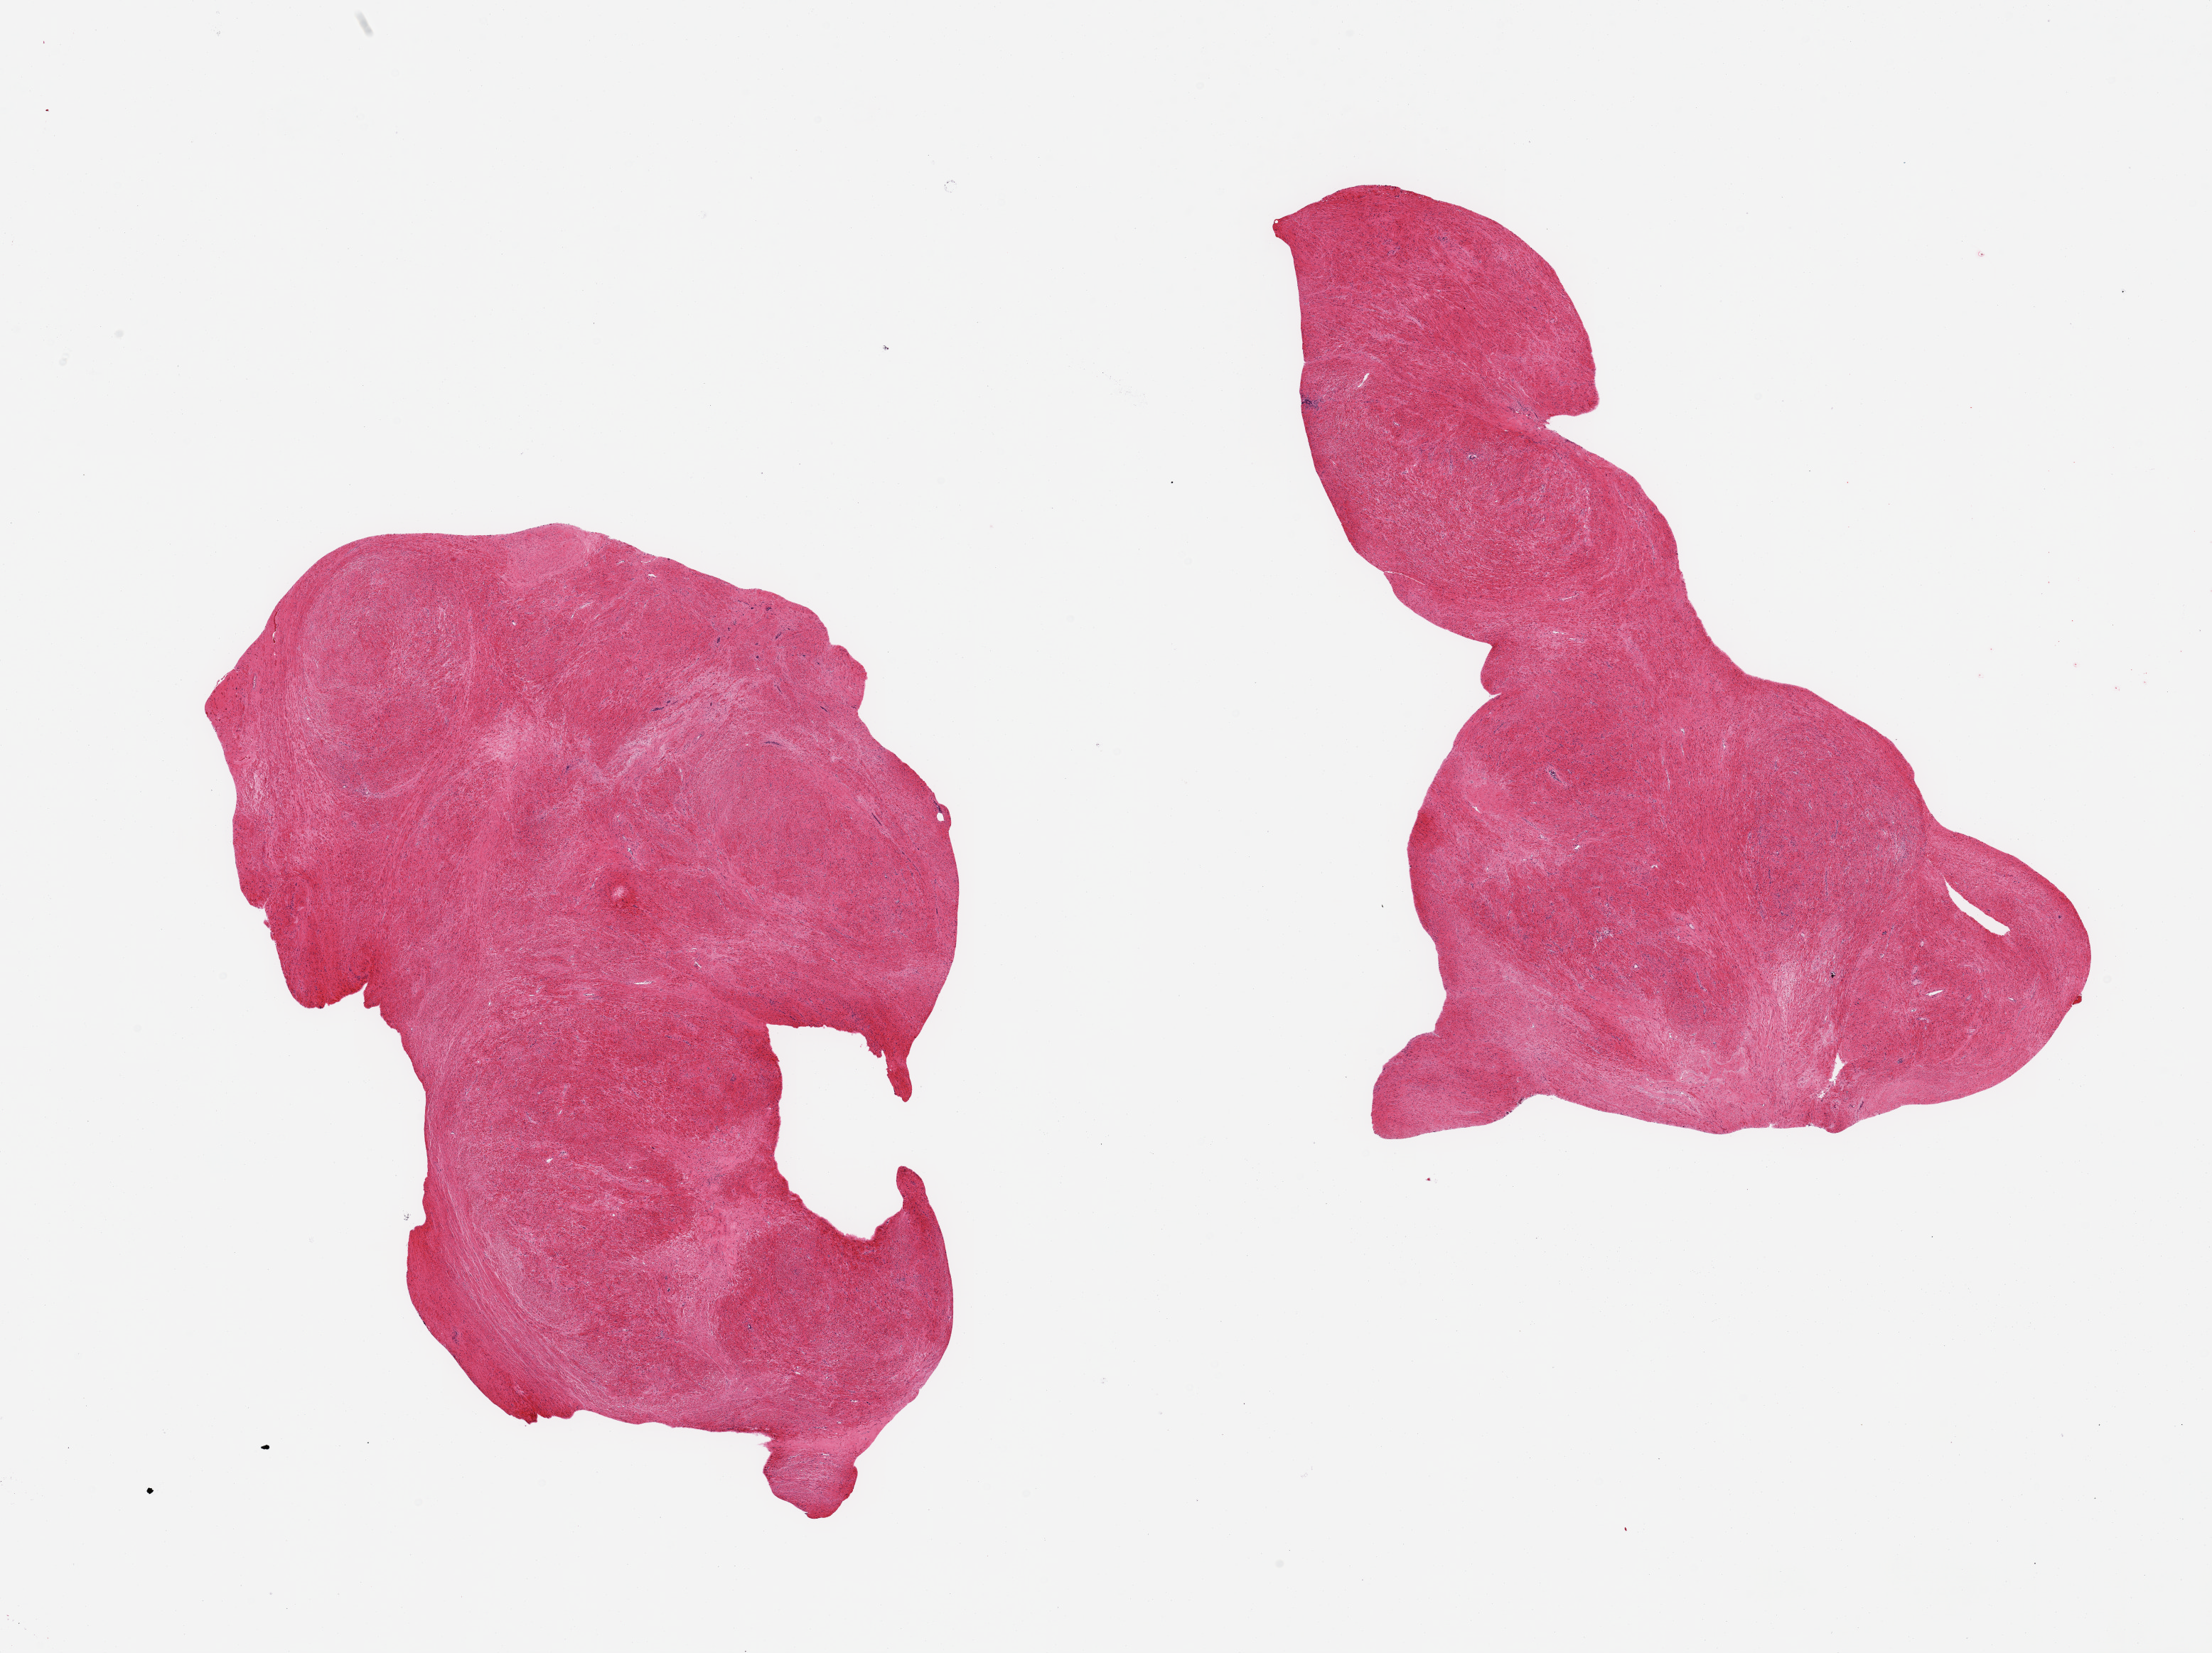
Hematoxylin and eosin (H&E) whole-slide image — shown as a low-resolution overview of the whole scanned area (about 24.6 x 18.4 mm, slide scanned at 20x); PAXgene-fixed, paraffin-embedded tissue; section of prostate (target tissue); donor tissue sample. Donor: male.
Review note (as recorded): 2 pieces, stromal hyperplasia, no glandular elements.